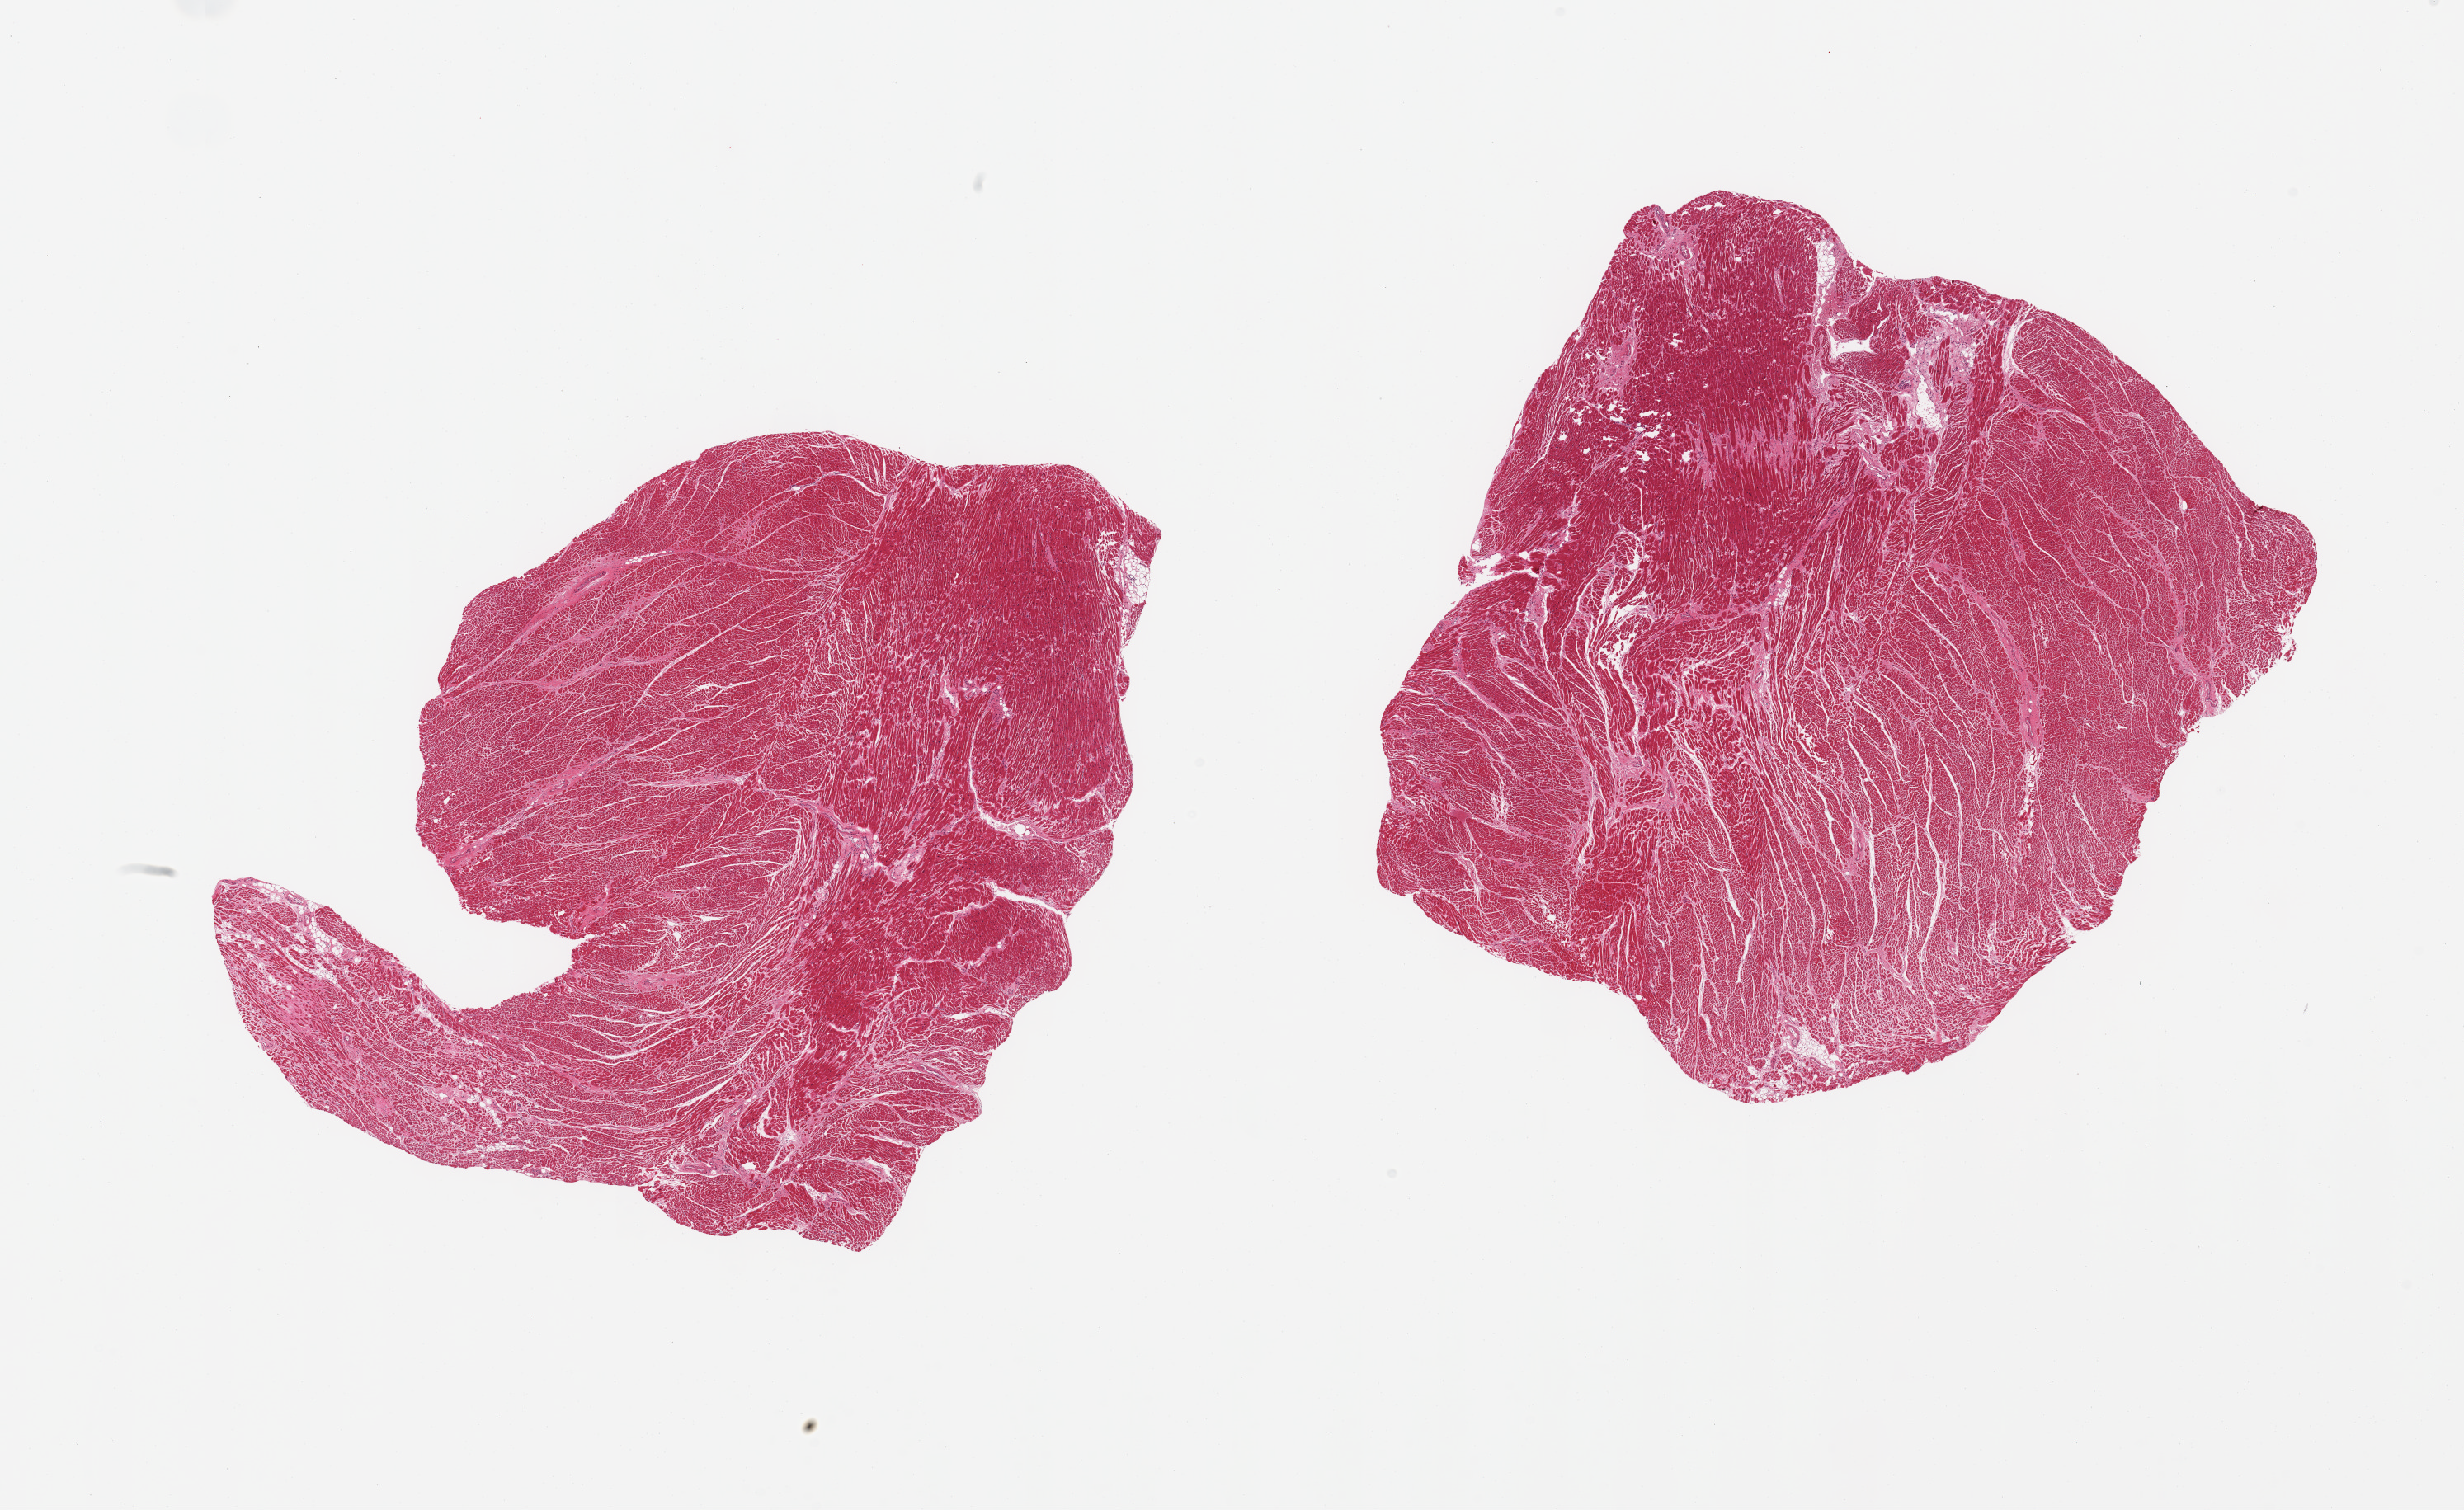
Digitized hematoxylin and eosin (H&E)-stained section, brightfield — a low-resolution overview of the entire scanned area, about 23.6 x 14.5 mm (slide scanned at 20x), PAXgene-fixed, paraffin-embedded tissue, sampled site (target tissue): heart, tissue donor sample. Female donor.
Review note (as recorded): 2 pieces, moderate chronic ischemic damage/ interstitial fibrosis.